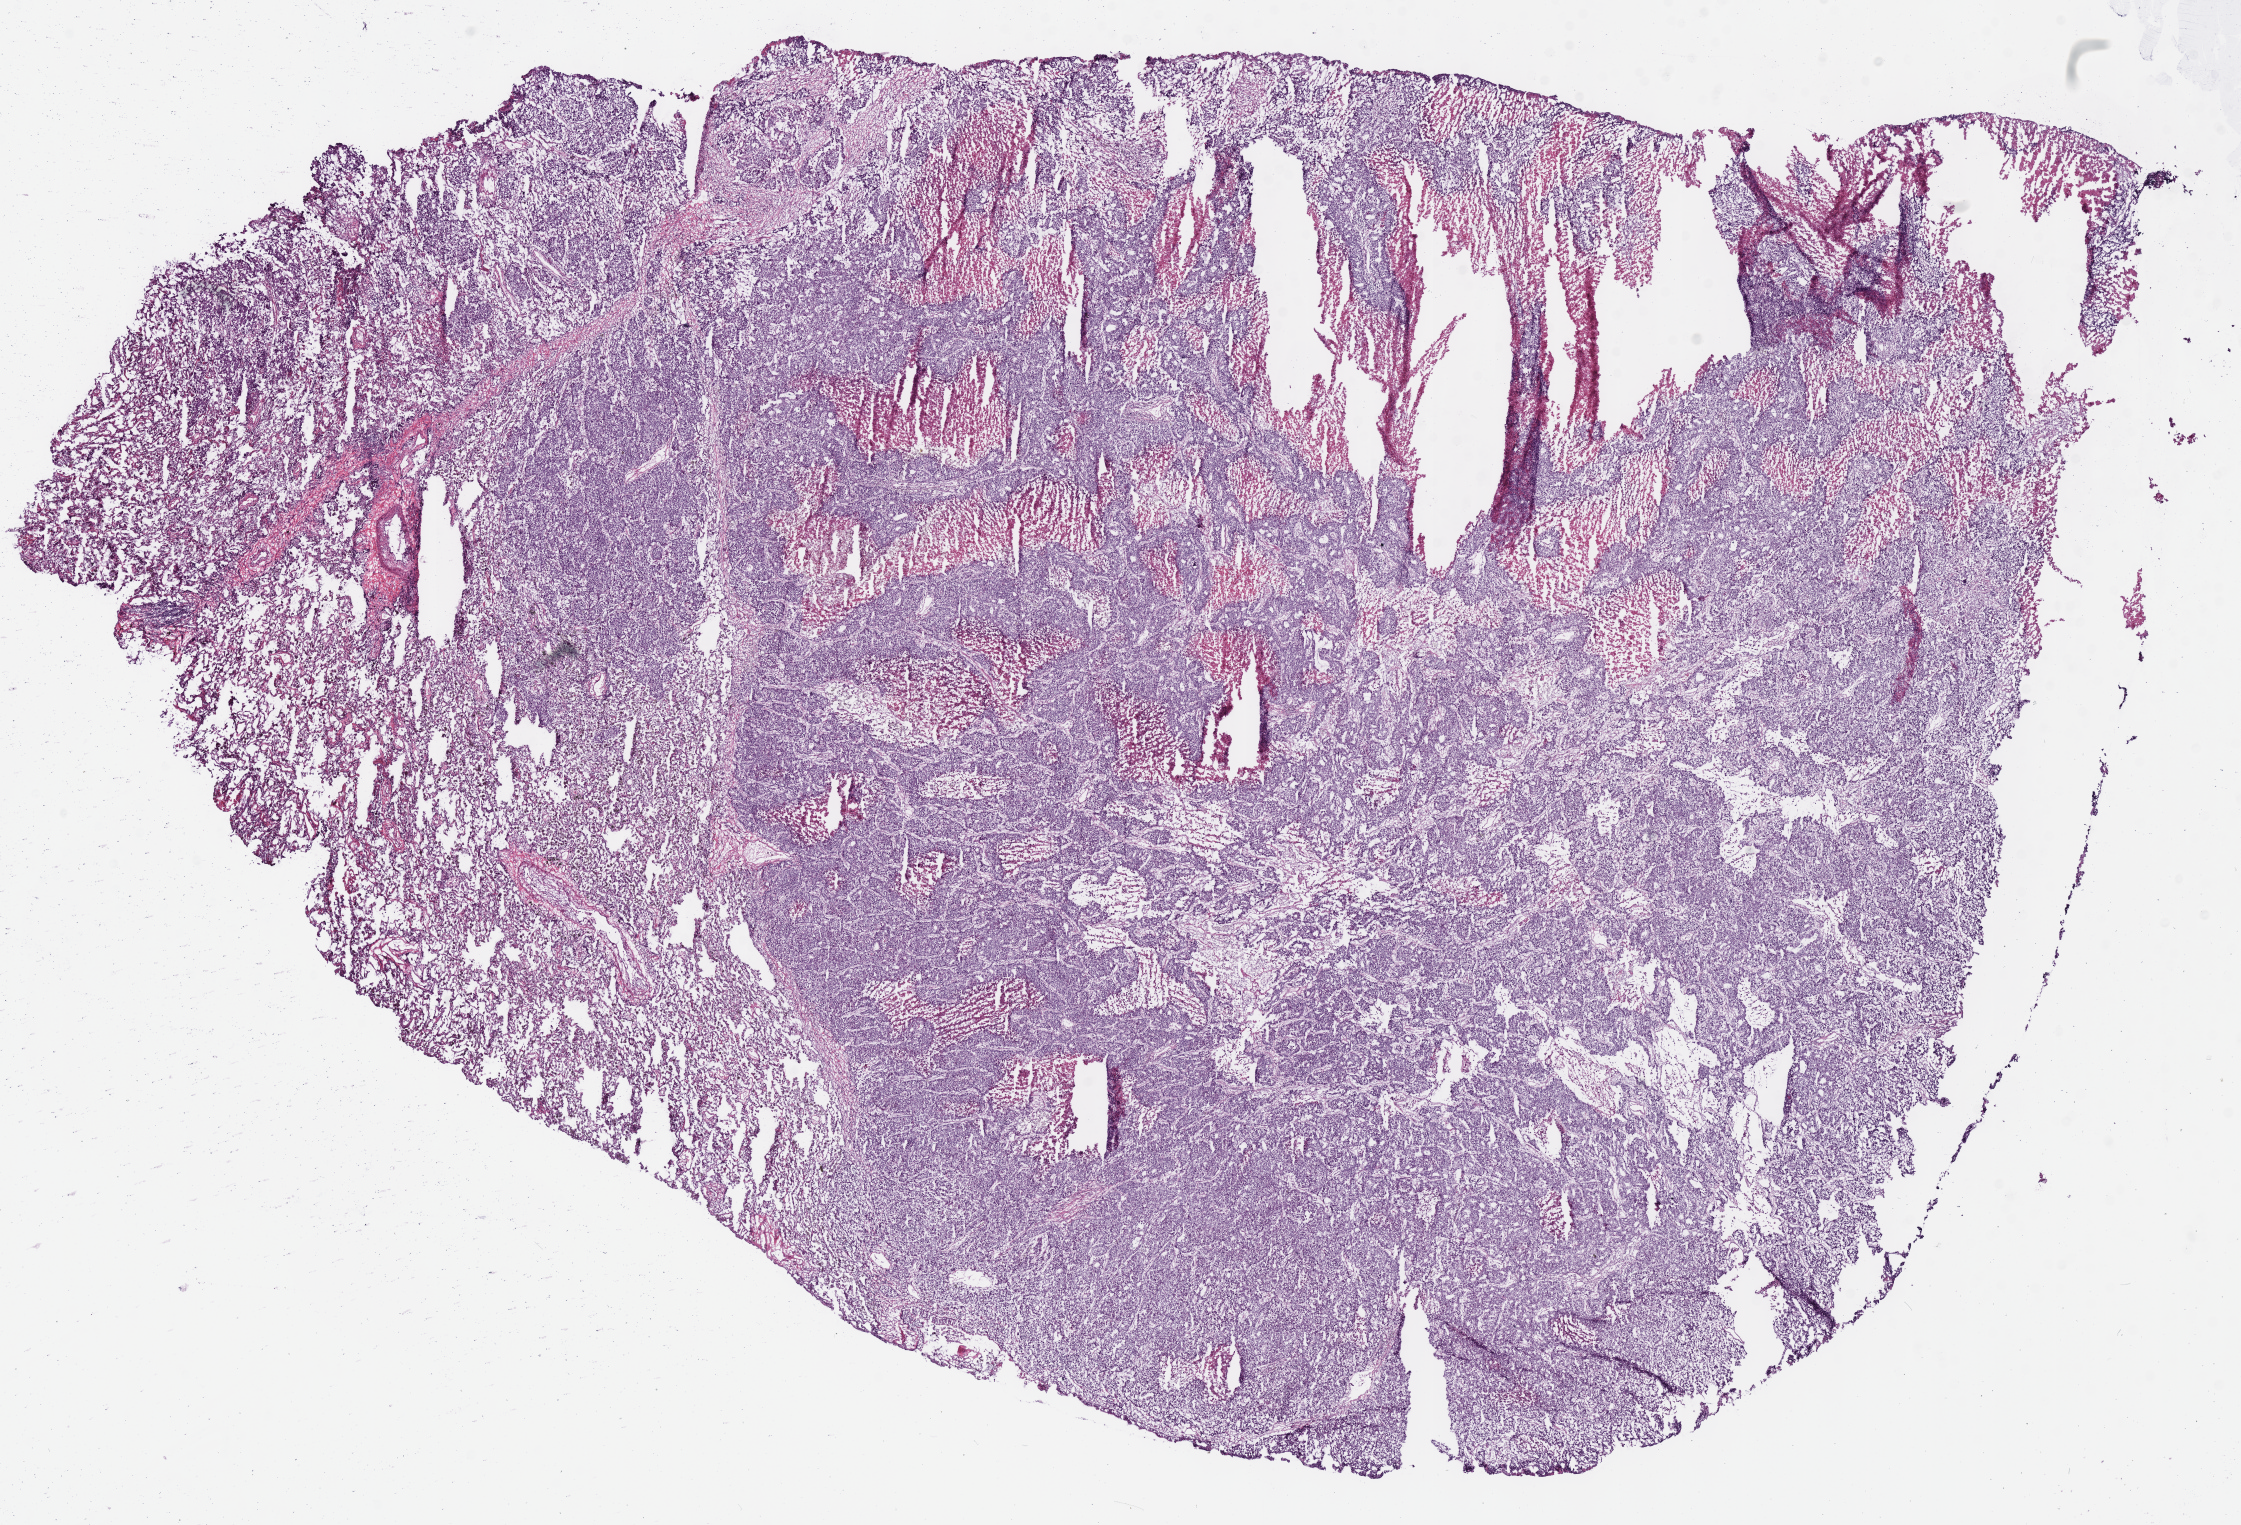
Whole-slide histology image, H&E-stained, whole scanned area (about 17.6 x 12.0 mm, from a 40x scan) shown as a low-resolution overview; frozen section from the top of the tissue portion; lung, primary tumour sample. Male, age 61 years at initial diagnosis. Composition of this section per pathologist review: tumour cells 68%, tumour nuclei 80%, normal cells 12%, stromal cells 5%, necrosis 15%. Infiltration values recorded for this section: lymphocyte infiltration 4%.
AJCC pathologic stage: IIB (7th edition). Histologic diagnosis: Acinar cell carcinoma (upper lobe, lung).